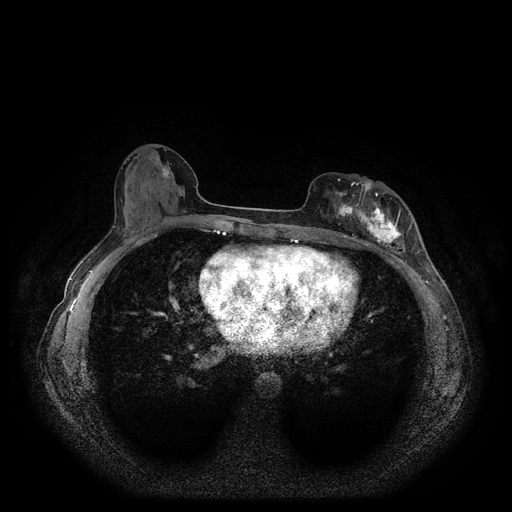
Breast MRI (dynamic contrast-enhanced, multi-phase), one axial slice. Slice 48 of 116 in the series (ordered by position). Dynamic contrast-enhanced series, time point 2 of 5 at this slice position (early post-contrast). 1.5 T. TE 2.6 ms, TR 5.3 ms. 512 × 512 image matrix, field of view 350 × 350 mm. Patient: female, 51 years.
Outlined on this slice (semi-automatically segmented with operator editing):
- breast lesion (labelled 'tumour' in the annotation; benign lesions carry a separate 'benign' label): bounding box <328,179,407,249> (left, top, right, bottom; pixels)
- breast lesion (labelled benign in the annotation): <162,164,171,180>